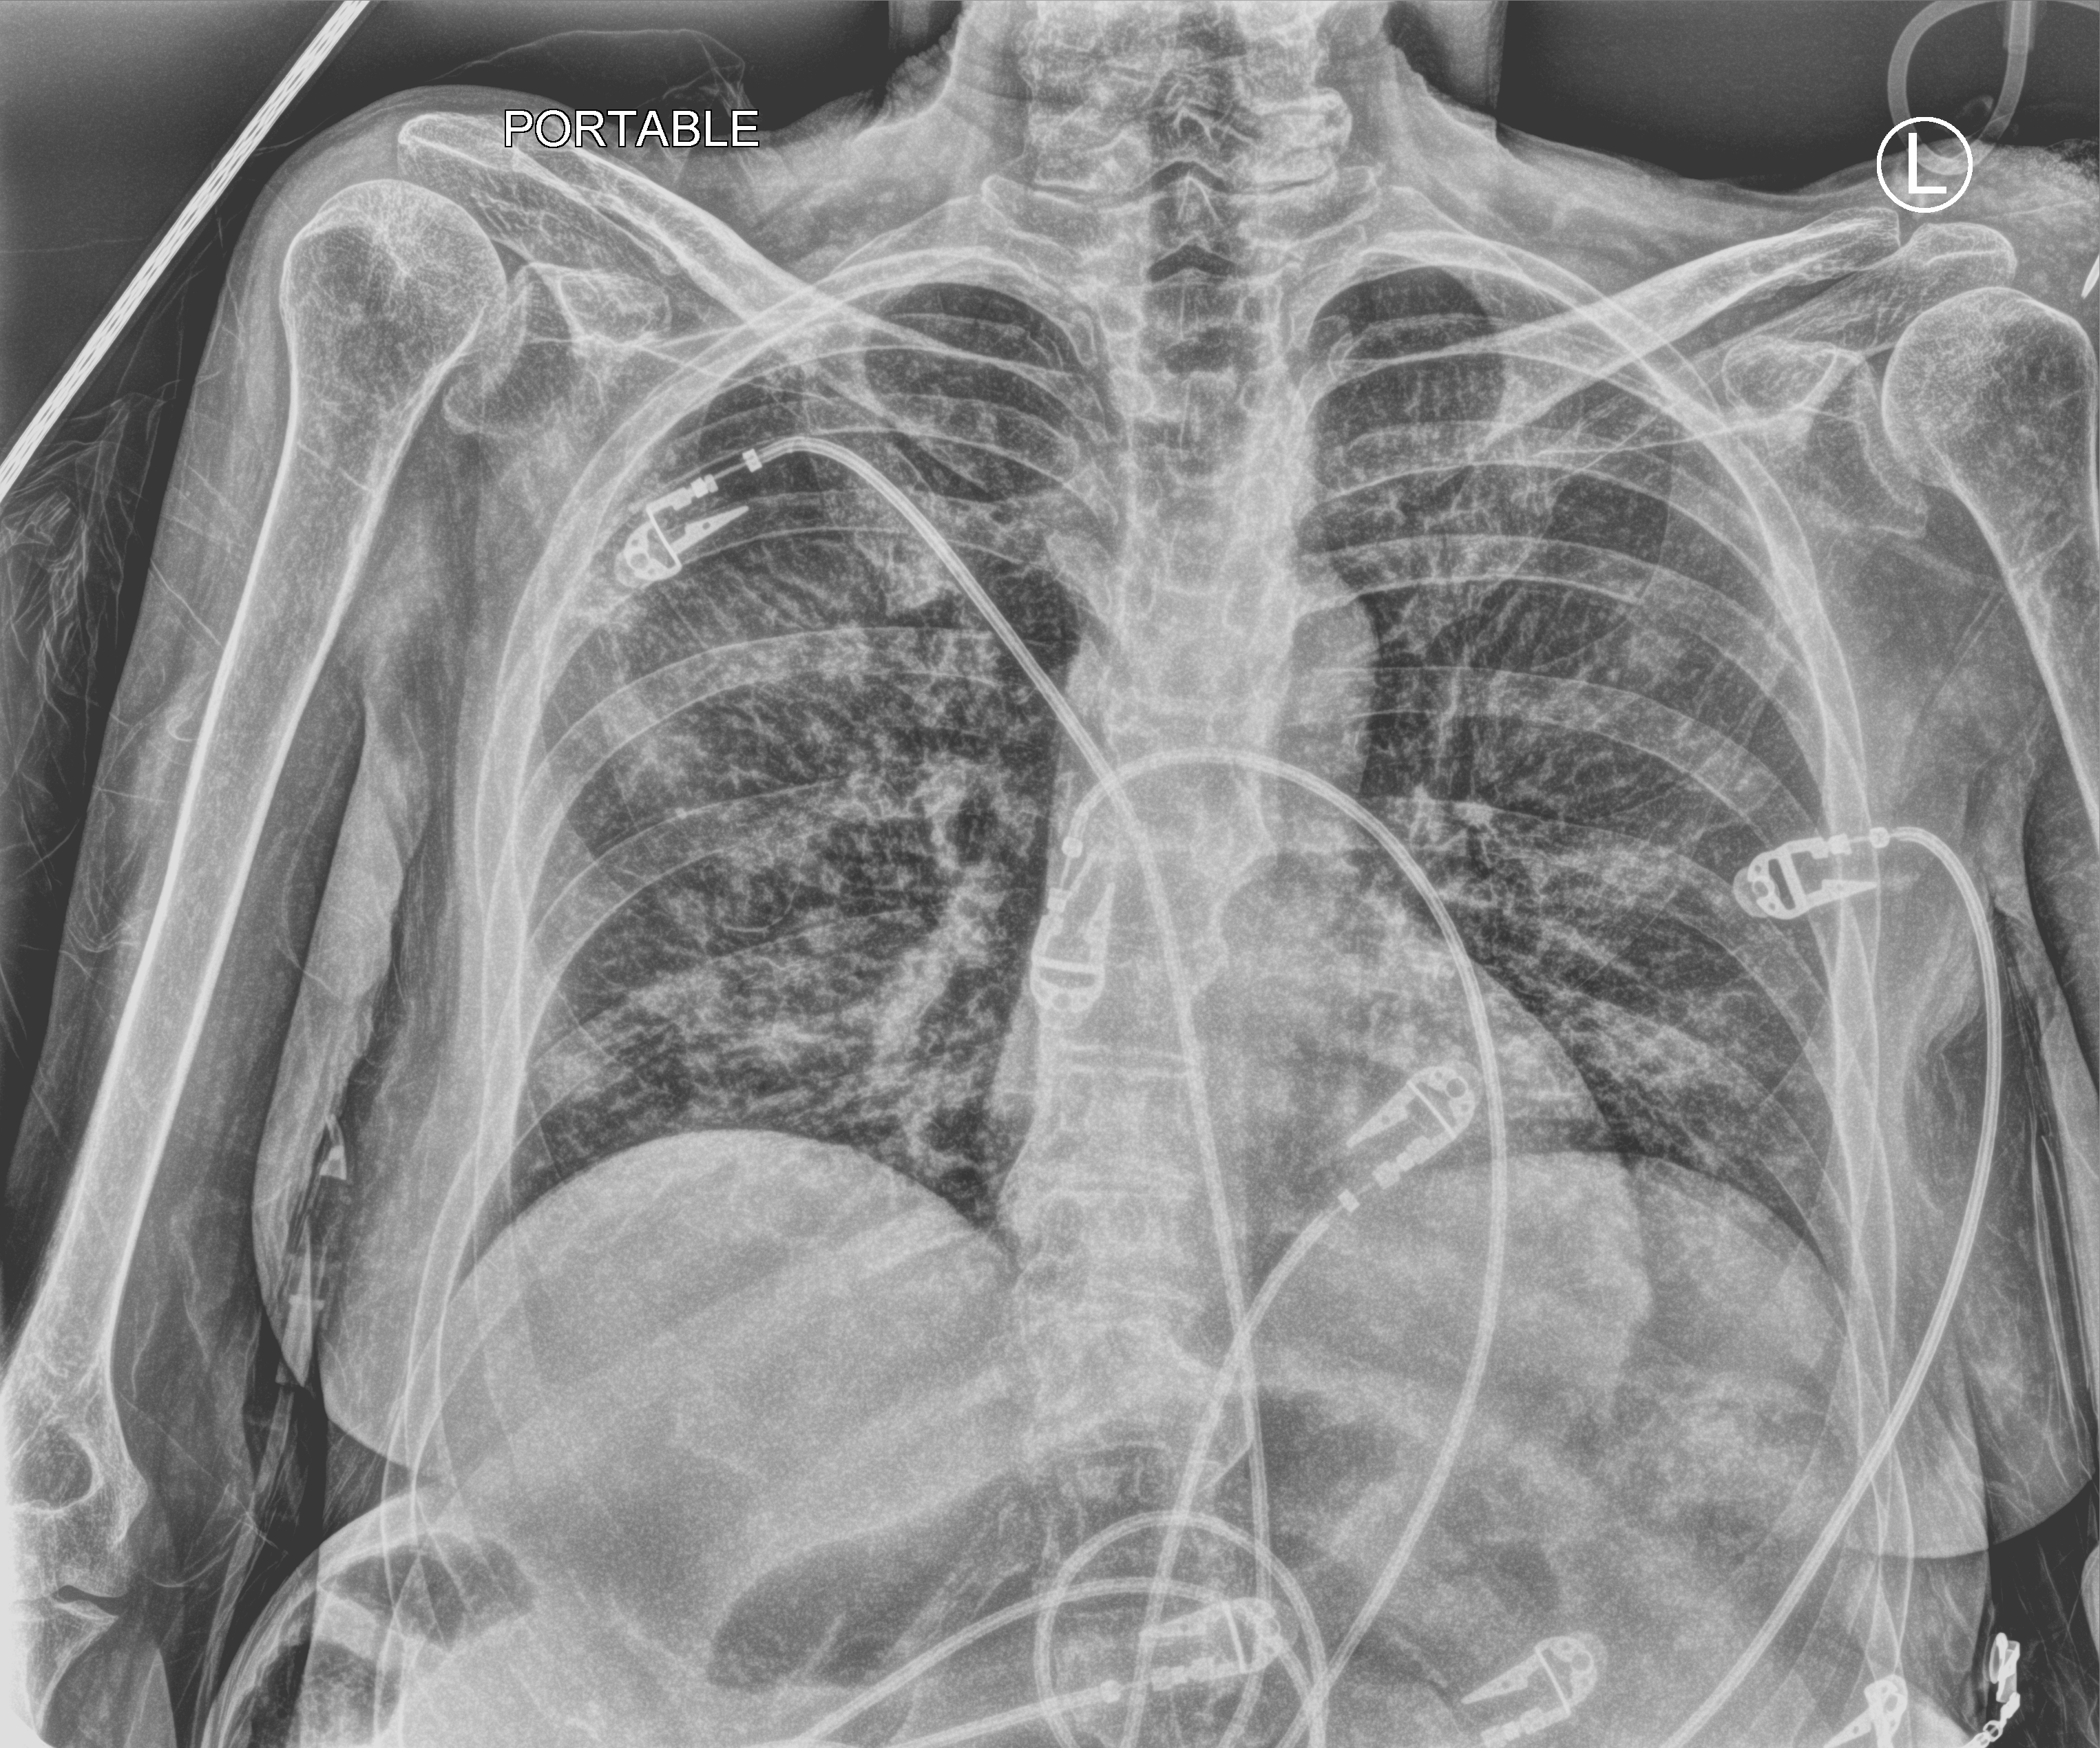
Portable chest radiograph, anteroposterior (AP) projection. Female patient hospitalised with COVID-19, age 60–74 years.
From the hospital-stay record, not from the radiograph (when in the stay this image was taken is not recorded): diabetes (admission record): no; length of hospital stay: 10 days; admitted to intensive care during this hospital stay: yes.